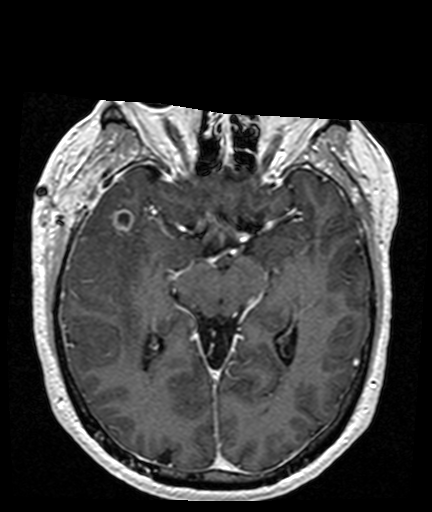
Brain MRI from a brain-tumour surgery series, one axial slice. Slice 97 of 176 in the series (ordered by position). T1-weighted post-contrast. 1 mm slice thickness. 432 × 512 image matrix, field of view 194 × 230 mm. Case-level facts recorded for this patient, not image findings: histopathology: Glioblastoma; WHO grade: 4; IDH mutation: no; tumour location: Right Frontal Temporal, Posterior Sylvian Fissure.
Annotated regions visible in this slice (expert manual segmentation):
- tumour: bounding box (x1, y1, x2, y2) in pixels: (112, 212, 133, 231)